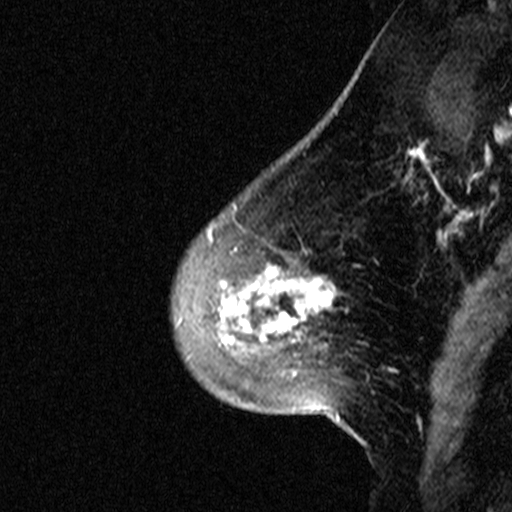
Breast MRI (dynamic contrast-enhanced), one sagittal slice; dynamic contrast-enhanced study with each time point stored as its own series, time point 2 of 3 at this slice position (early post-contrast, ordered by acquisition time); 1.5 T; TE 4.5 ms, TR 11 ms; 512 × 512 image matrix, field of view 200 × 200 mm. Patient: female, 46 years. Case-level facts recorded for this patient, not image findings: setting: breast cancer imaged before/during neoadjuvant chemotherapy; receptor status: HER2-positive.
Annotated regions visible in this slice (semi-automatic segmentation, software-assisted and operator-edited):
- analysis volume of interest (the breast-tissue region the enhancement analysis was run in; not a lesion): bounding box (x1, y1, x2, y2) in pixels: (171, 172, 359, 393)
- tumour enhancement mask (voxels above the 90 % enhancement threshold inside the analysis volume of interest): (209, 227, 333, 342)